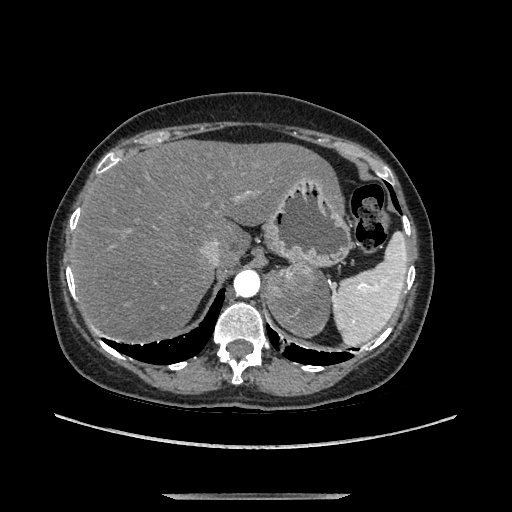
Contrast-enhanced abdominal CT, one axial slice. Position 104 of 169 along the scan axis. Soft-tissue window (W 400 / L 40 HU). 1.25 mm slice thickness. 512 × 512 image matrix. Female patient. From the clinical record (not read from this slice): diagnosis: adrenocortical carcinoma; tumour side: left adrenal; tumour size at pathology: 9 cm; Ki-67 index: 2 %; stage (as recorded): 3.
Outlined on this slice (semi-automatic segmentation, software-assisted and operator-edited):
- mass: bounding box [x1, y1, x2, y2] px = [264, 261, 328, 334]